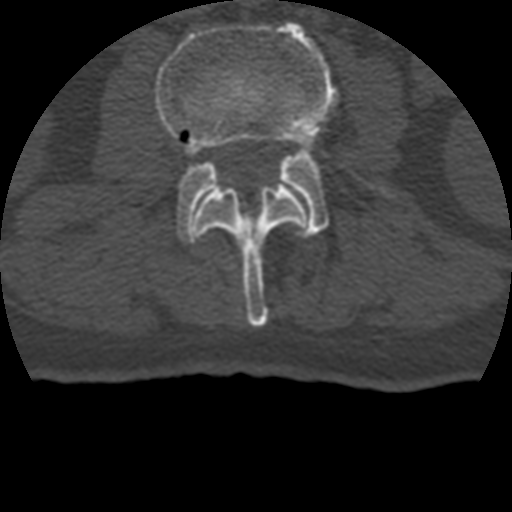
CT including the spine, one axial slice; slice 101 of 399 in the series (ordered by position); 120 kVp; bone window (W 1800 / L 400 HU); 512 × 512 image matrix, field of view 160 × 160 mm. Patient age 69 years. Case-level facts recorded for this patient, not image findings: primary cancer: prostate.
Annotated regions visible in this slice (semi-automatic segmentation, software-assisted and operator-edited):
- L2 vertebra: bounding box <193,186,309,327> (left, top, right, bottom; pixels)
- L3 vertebra: <155,21,401,238>